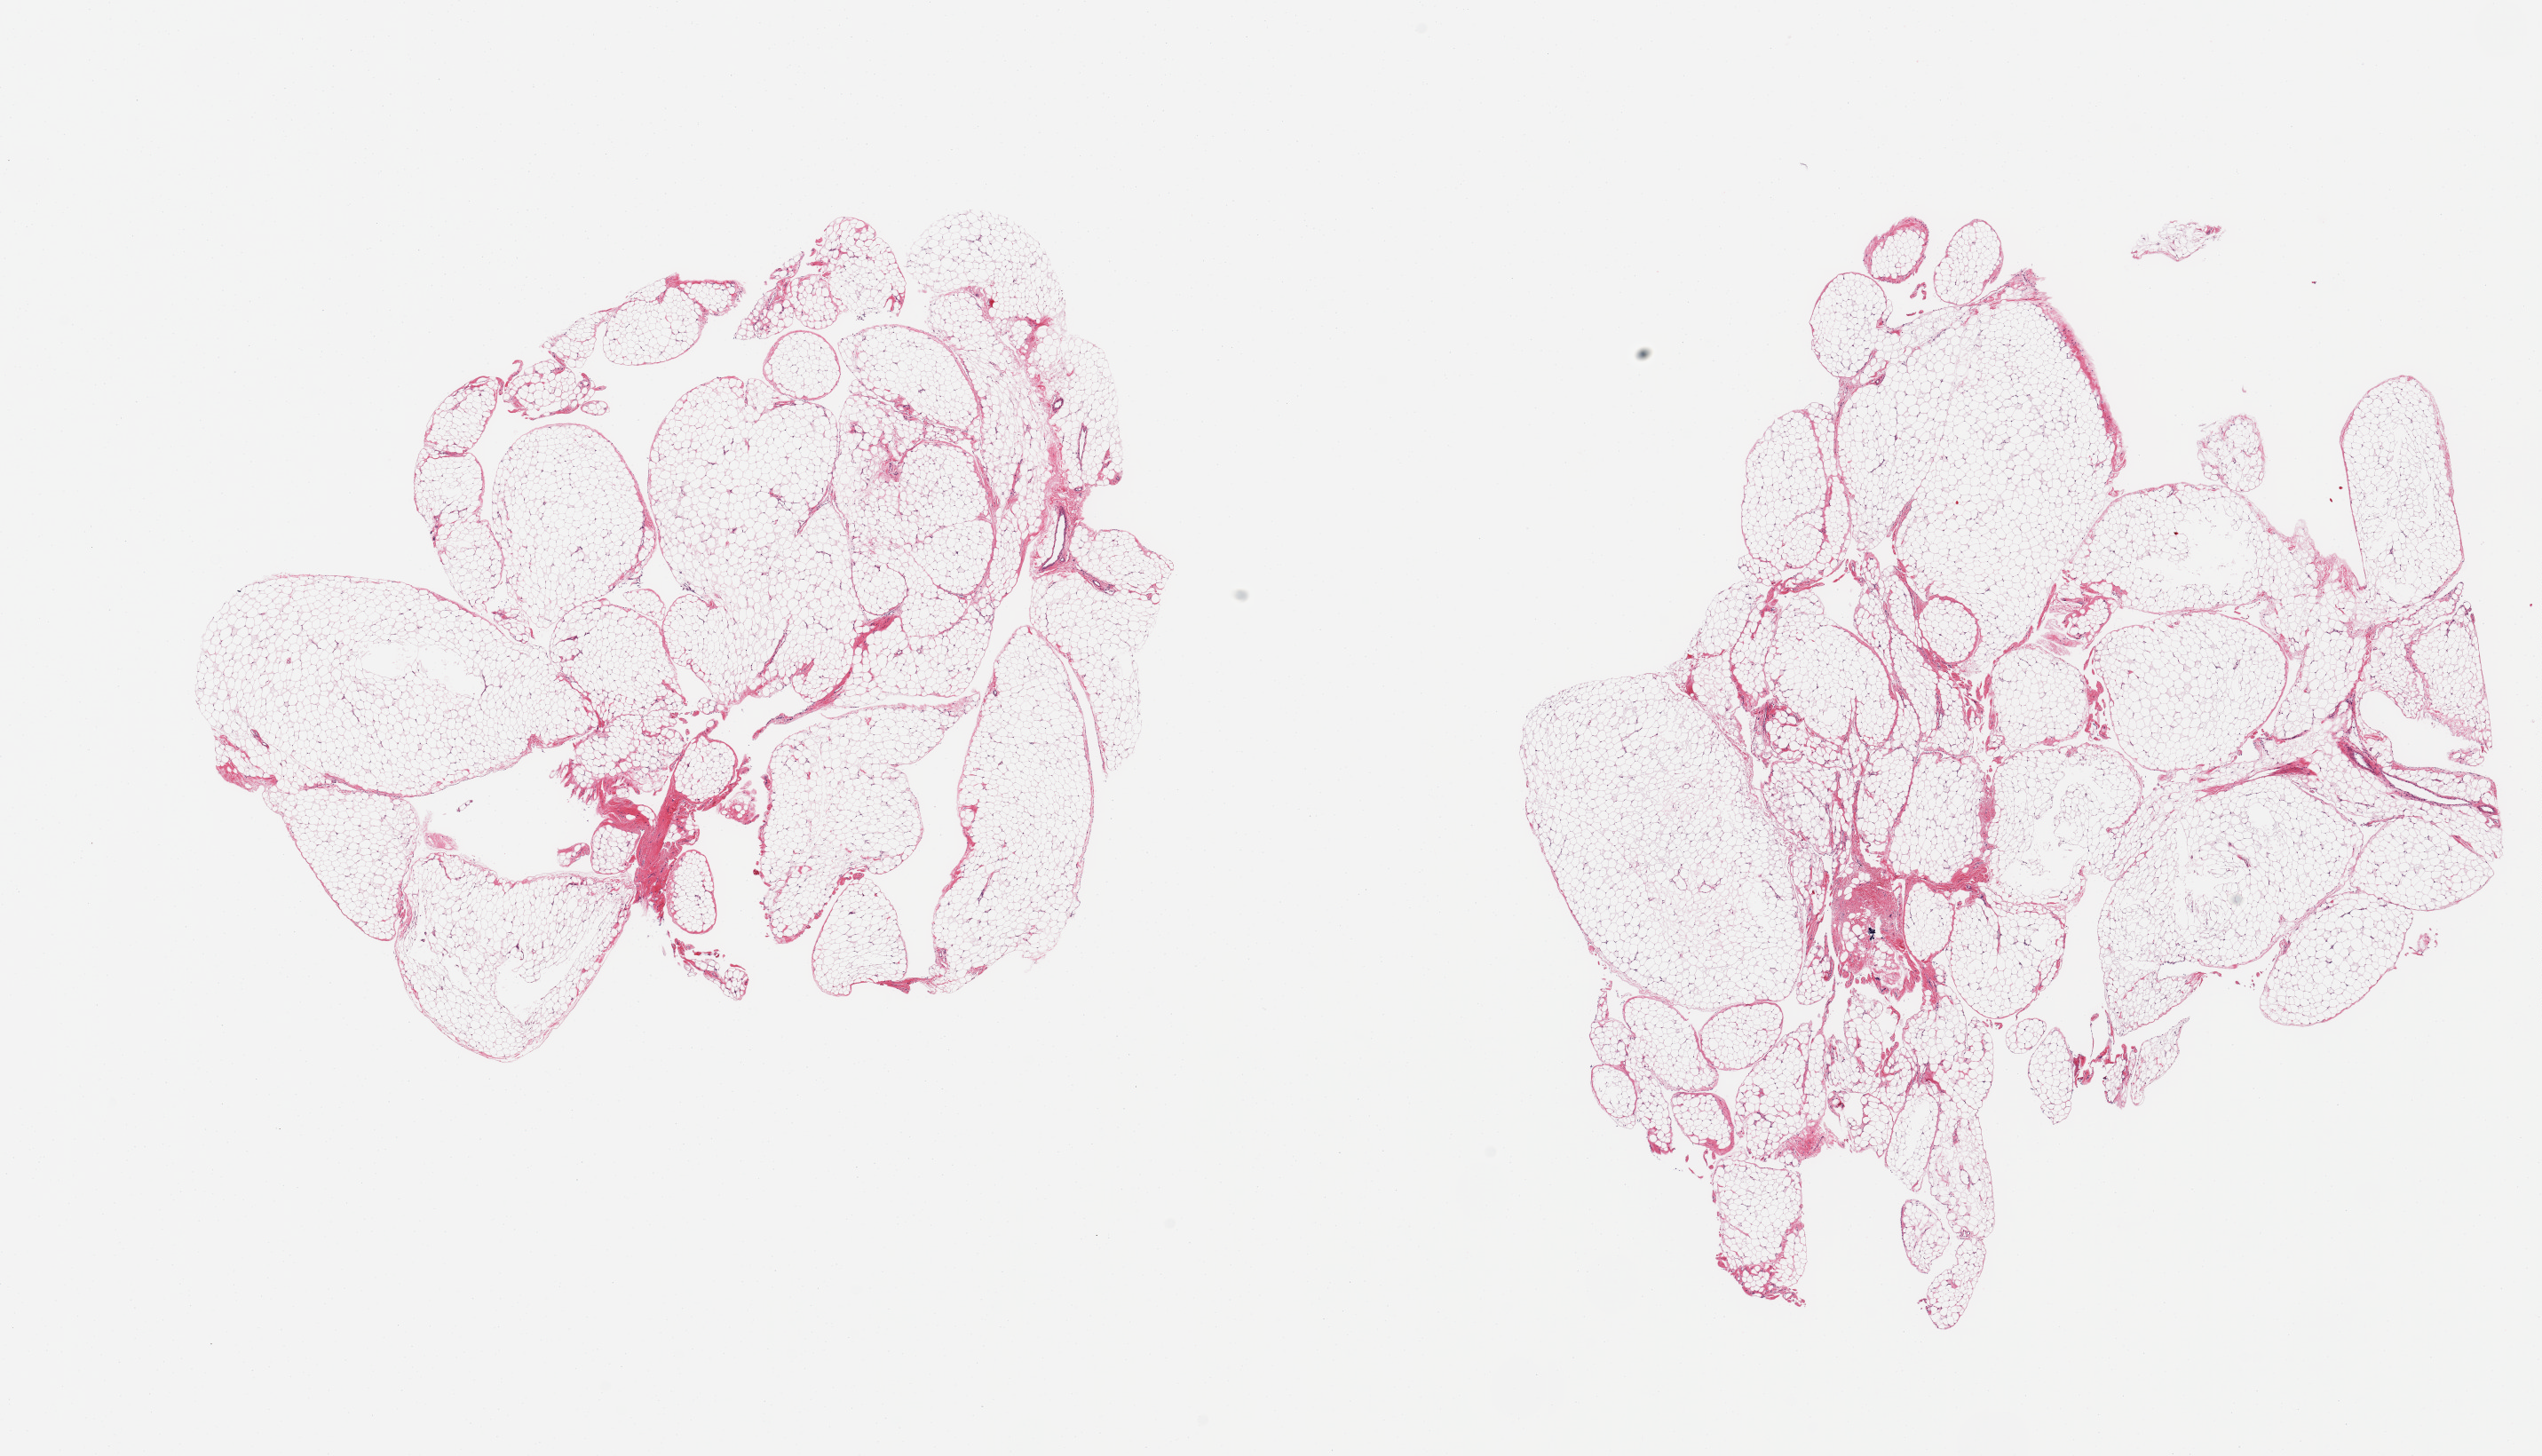
Whole-slide image, hematoxylin and eosin (H&E) stain — whole scanned area (about 22.6 x 13.0 mm) shown as a low-resolution overview; PAXgene-fixed paraffin-embedded (PFPE) section; sampled site (target tissue): omentum; donor tissue sample. Male donor.
- pathologist's review note for this sample: 2 pieces; lobulated mature adipose tissue